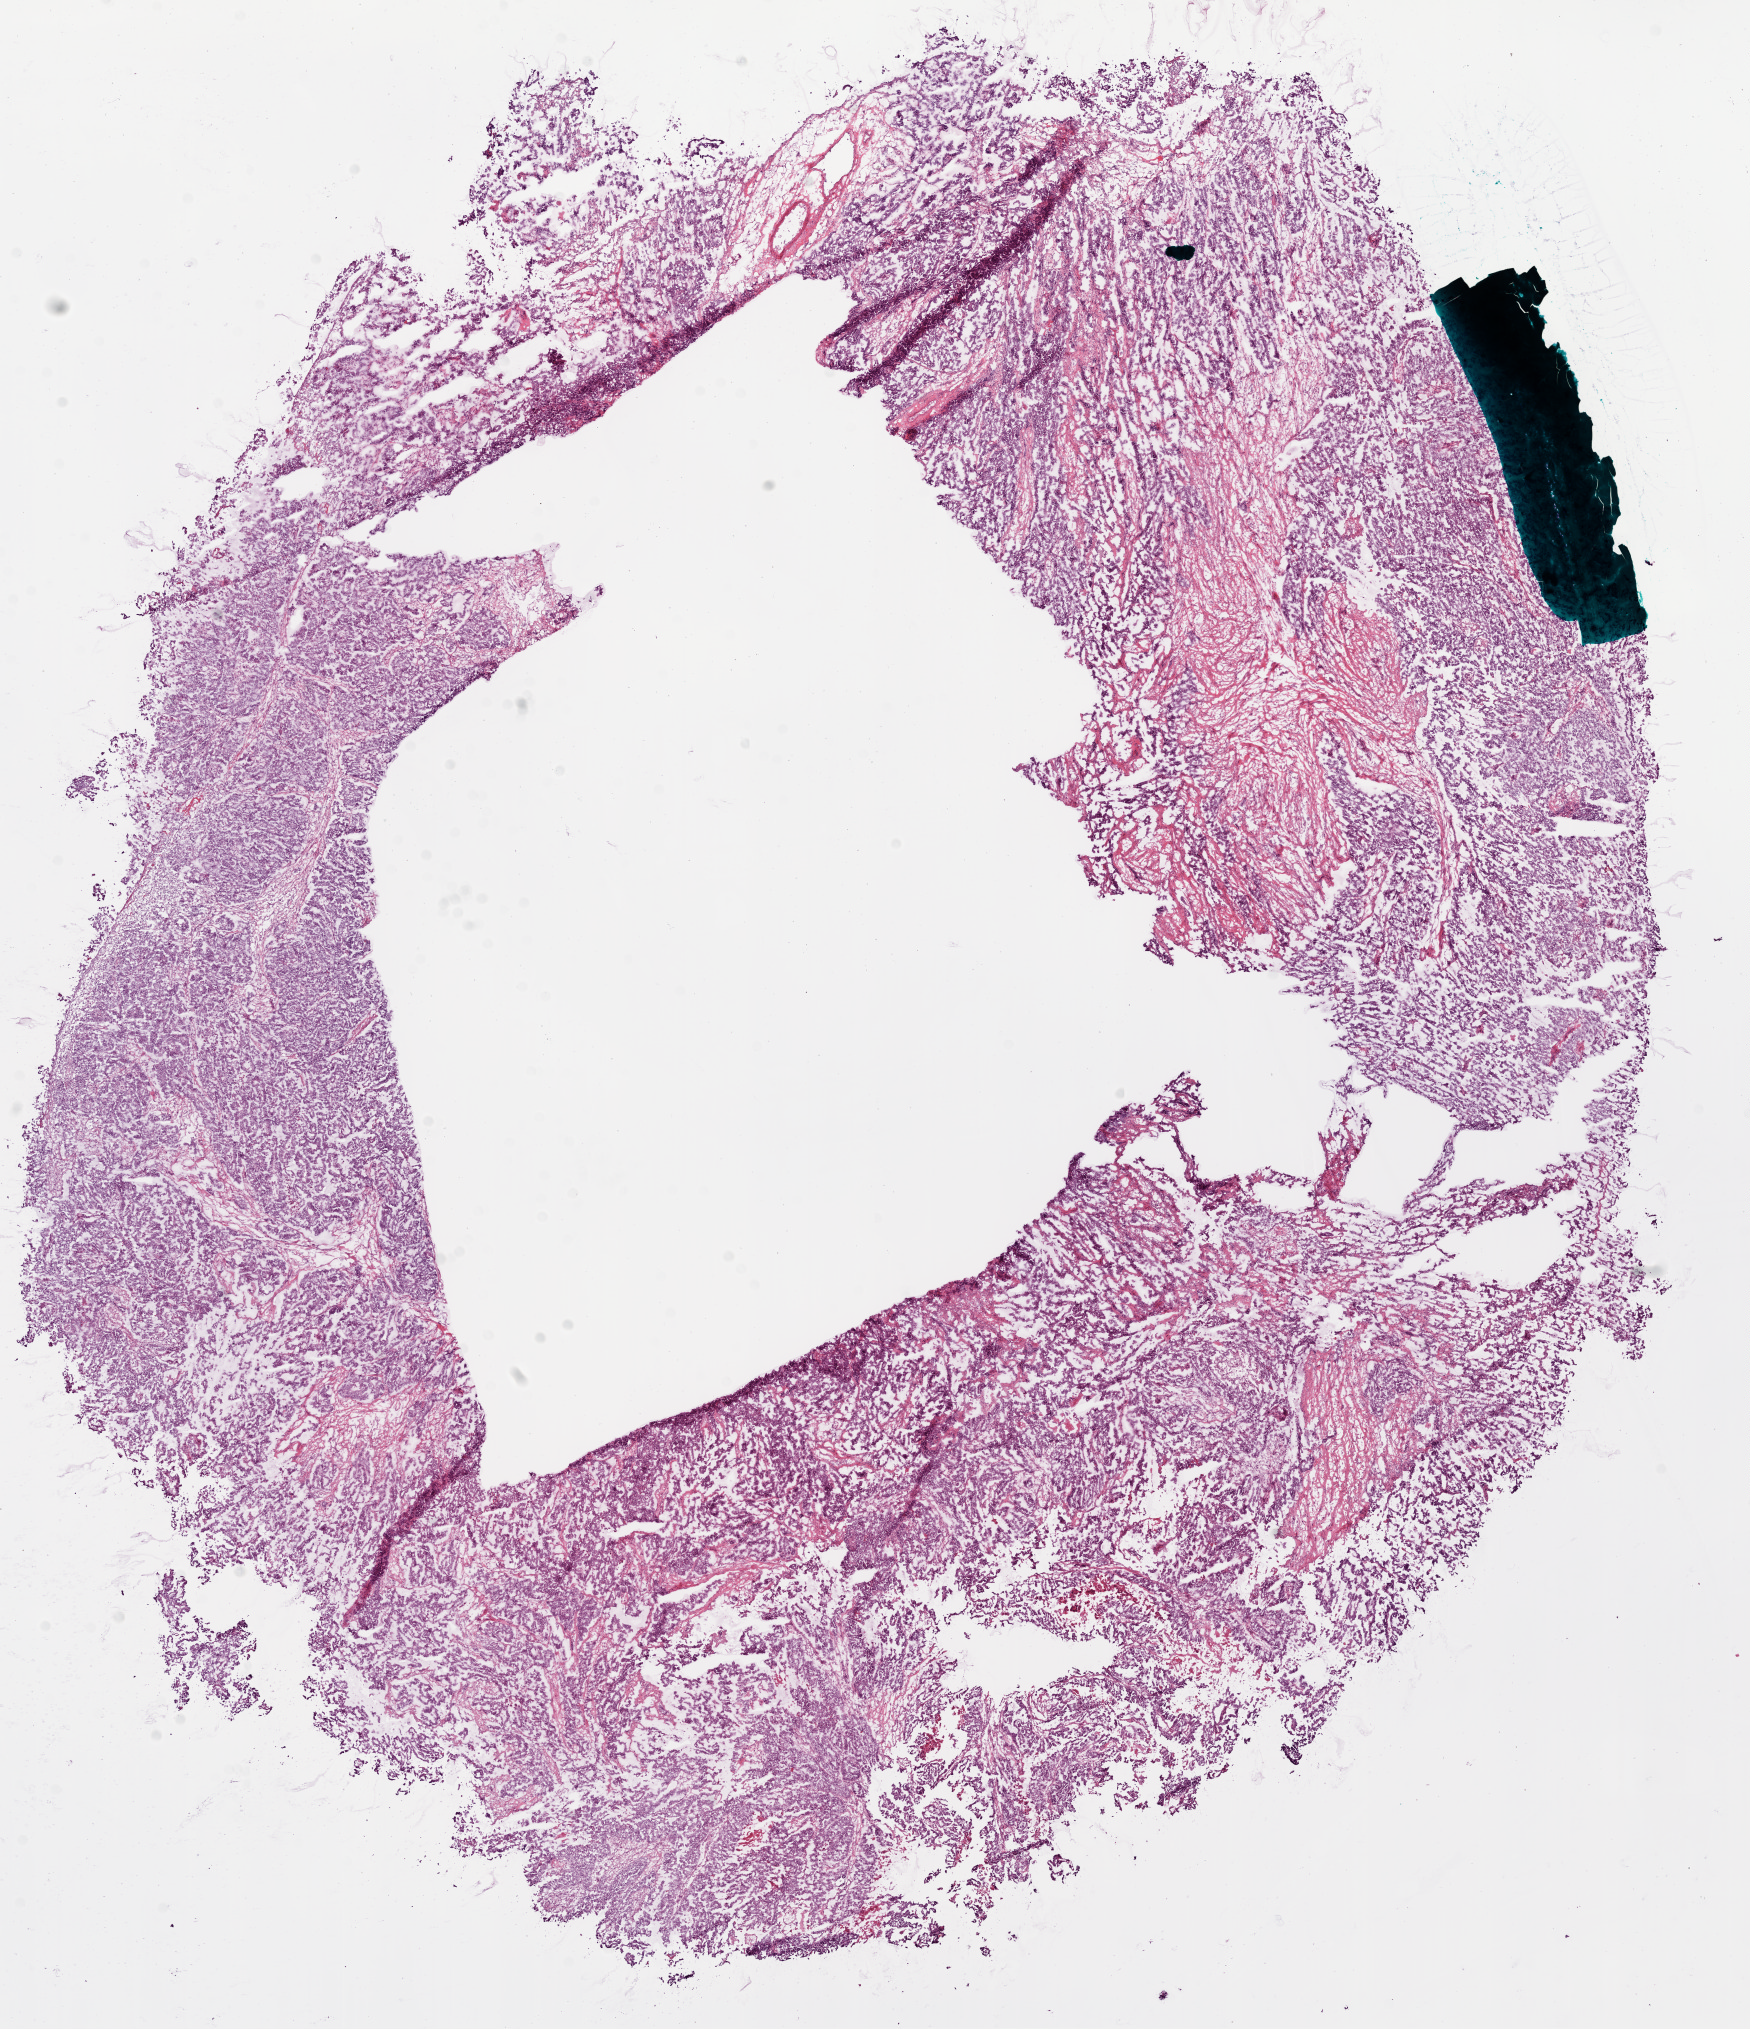
Whole-slide histology image, H&E-stained — a low-resolution overview of the entire scanned area, about 14.0 x 16.3 mm (acquisition: 20x scan), frozen section from the bottom of the tissue portion, sample: primary tumour, ovary. Female patient; age at initial diagnosis 41 years. Histologic grade: G3 (poorly differentiated). Pathologist review of this section (percent, as recorded): tumour cells 89%, tumour nuclei 90%, normal cells 0%, stromal cells 10%, necrosis 1%.
Histologic diagnosis: Serous cystadenocarcinoma, NOS. FIGO stage: IIIC.